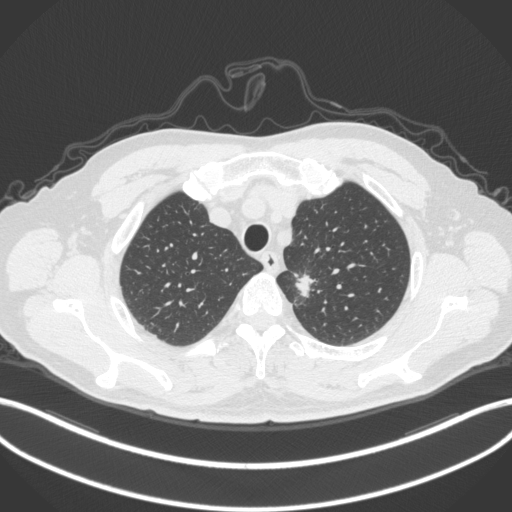
Chest CT, one axial slice. Position 310 of 382 along the scan axis. Reconstruction kernel B31f. 120 kVp. Lung window (W 1500 / L -600 HU). 1 mm slice thickness. 512 × 512 image matrix, field of view 400 × 400 mm. Male patient, age 64 years. Case-level facts recorded for this patient, not image findings: clinical TNM (as recorded): T1c N0 M0.
Outlined on this slice (rectangle marked by the reading radiologist):
- lung tumour (recorded histology: adenocarcinoma): bounding box (x1, y1, x2, y2) in pixels: (289, 268, 319, 308)